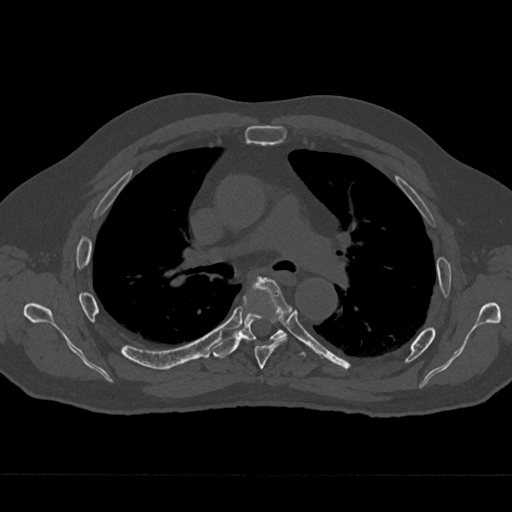
CT including the spine, one axial slice. Slice 451 of 797 in the series (ordered by position). Reconstruction kernel Br40s/3. Bone window (W 1800 / L 400 HU). 512 × 512 image matrix, field of view 377 × 377 mm. Male patient, age 75 years. From the clinical record (not read from this slice): primary cancer: renal.
Structures marked on this image (semi-automatically segmented with operator editing):
- T5 vertebra: bounding box [x1, y1, x2, y2] px = [253, 278, 292, 369]
- T6 vertebra: [213, 277, 305, 358]